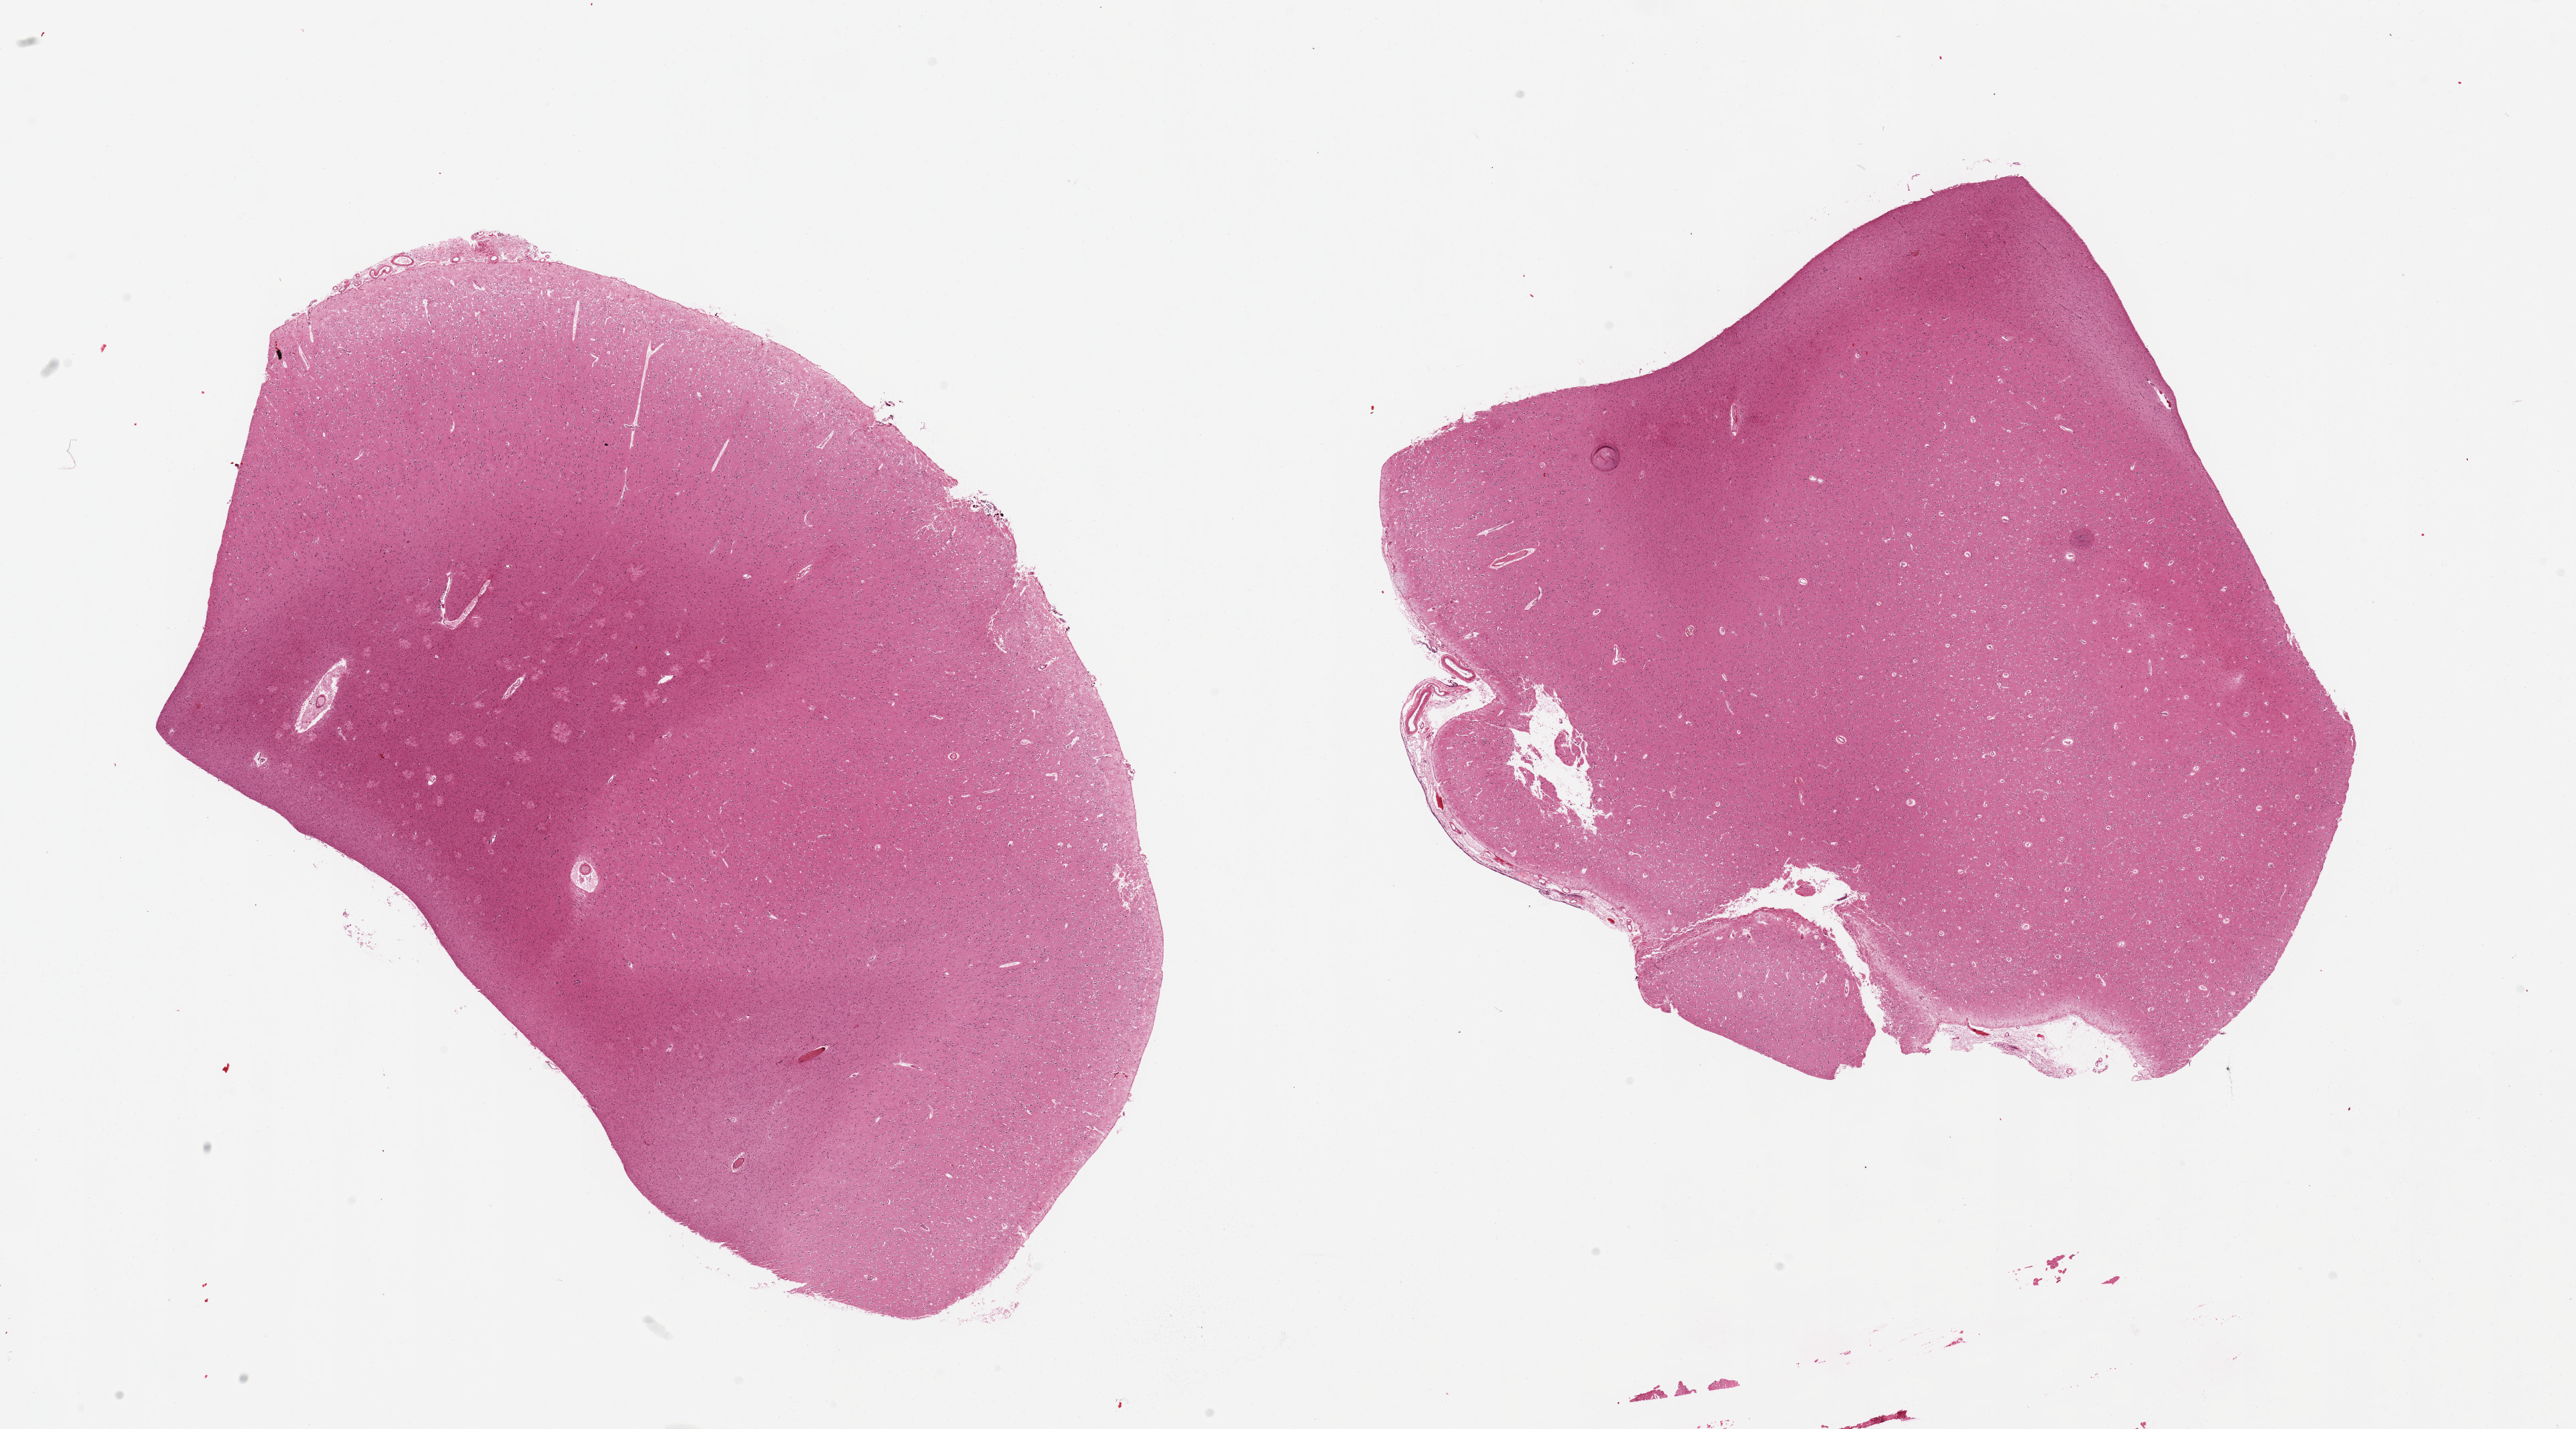
Hematoxylin and eosin (H&E) whole-slide image, low-resolution overview of the scanned area, about 30.5 x 16.9 mm. PAXgene-fixed, paraffin-embedded tissue. Sampled site (target tissue): cerebral cortex. Tissue donor sample. Male donor.
Review note (as recorded): 2 pieces.